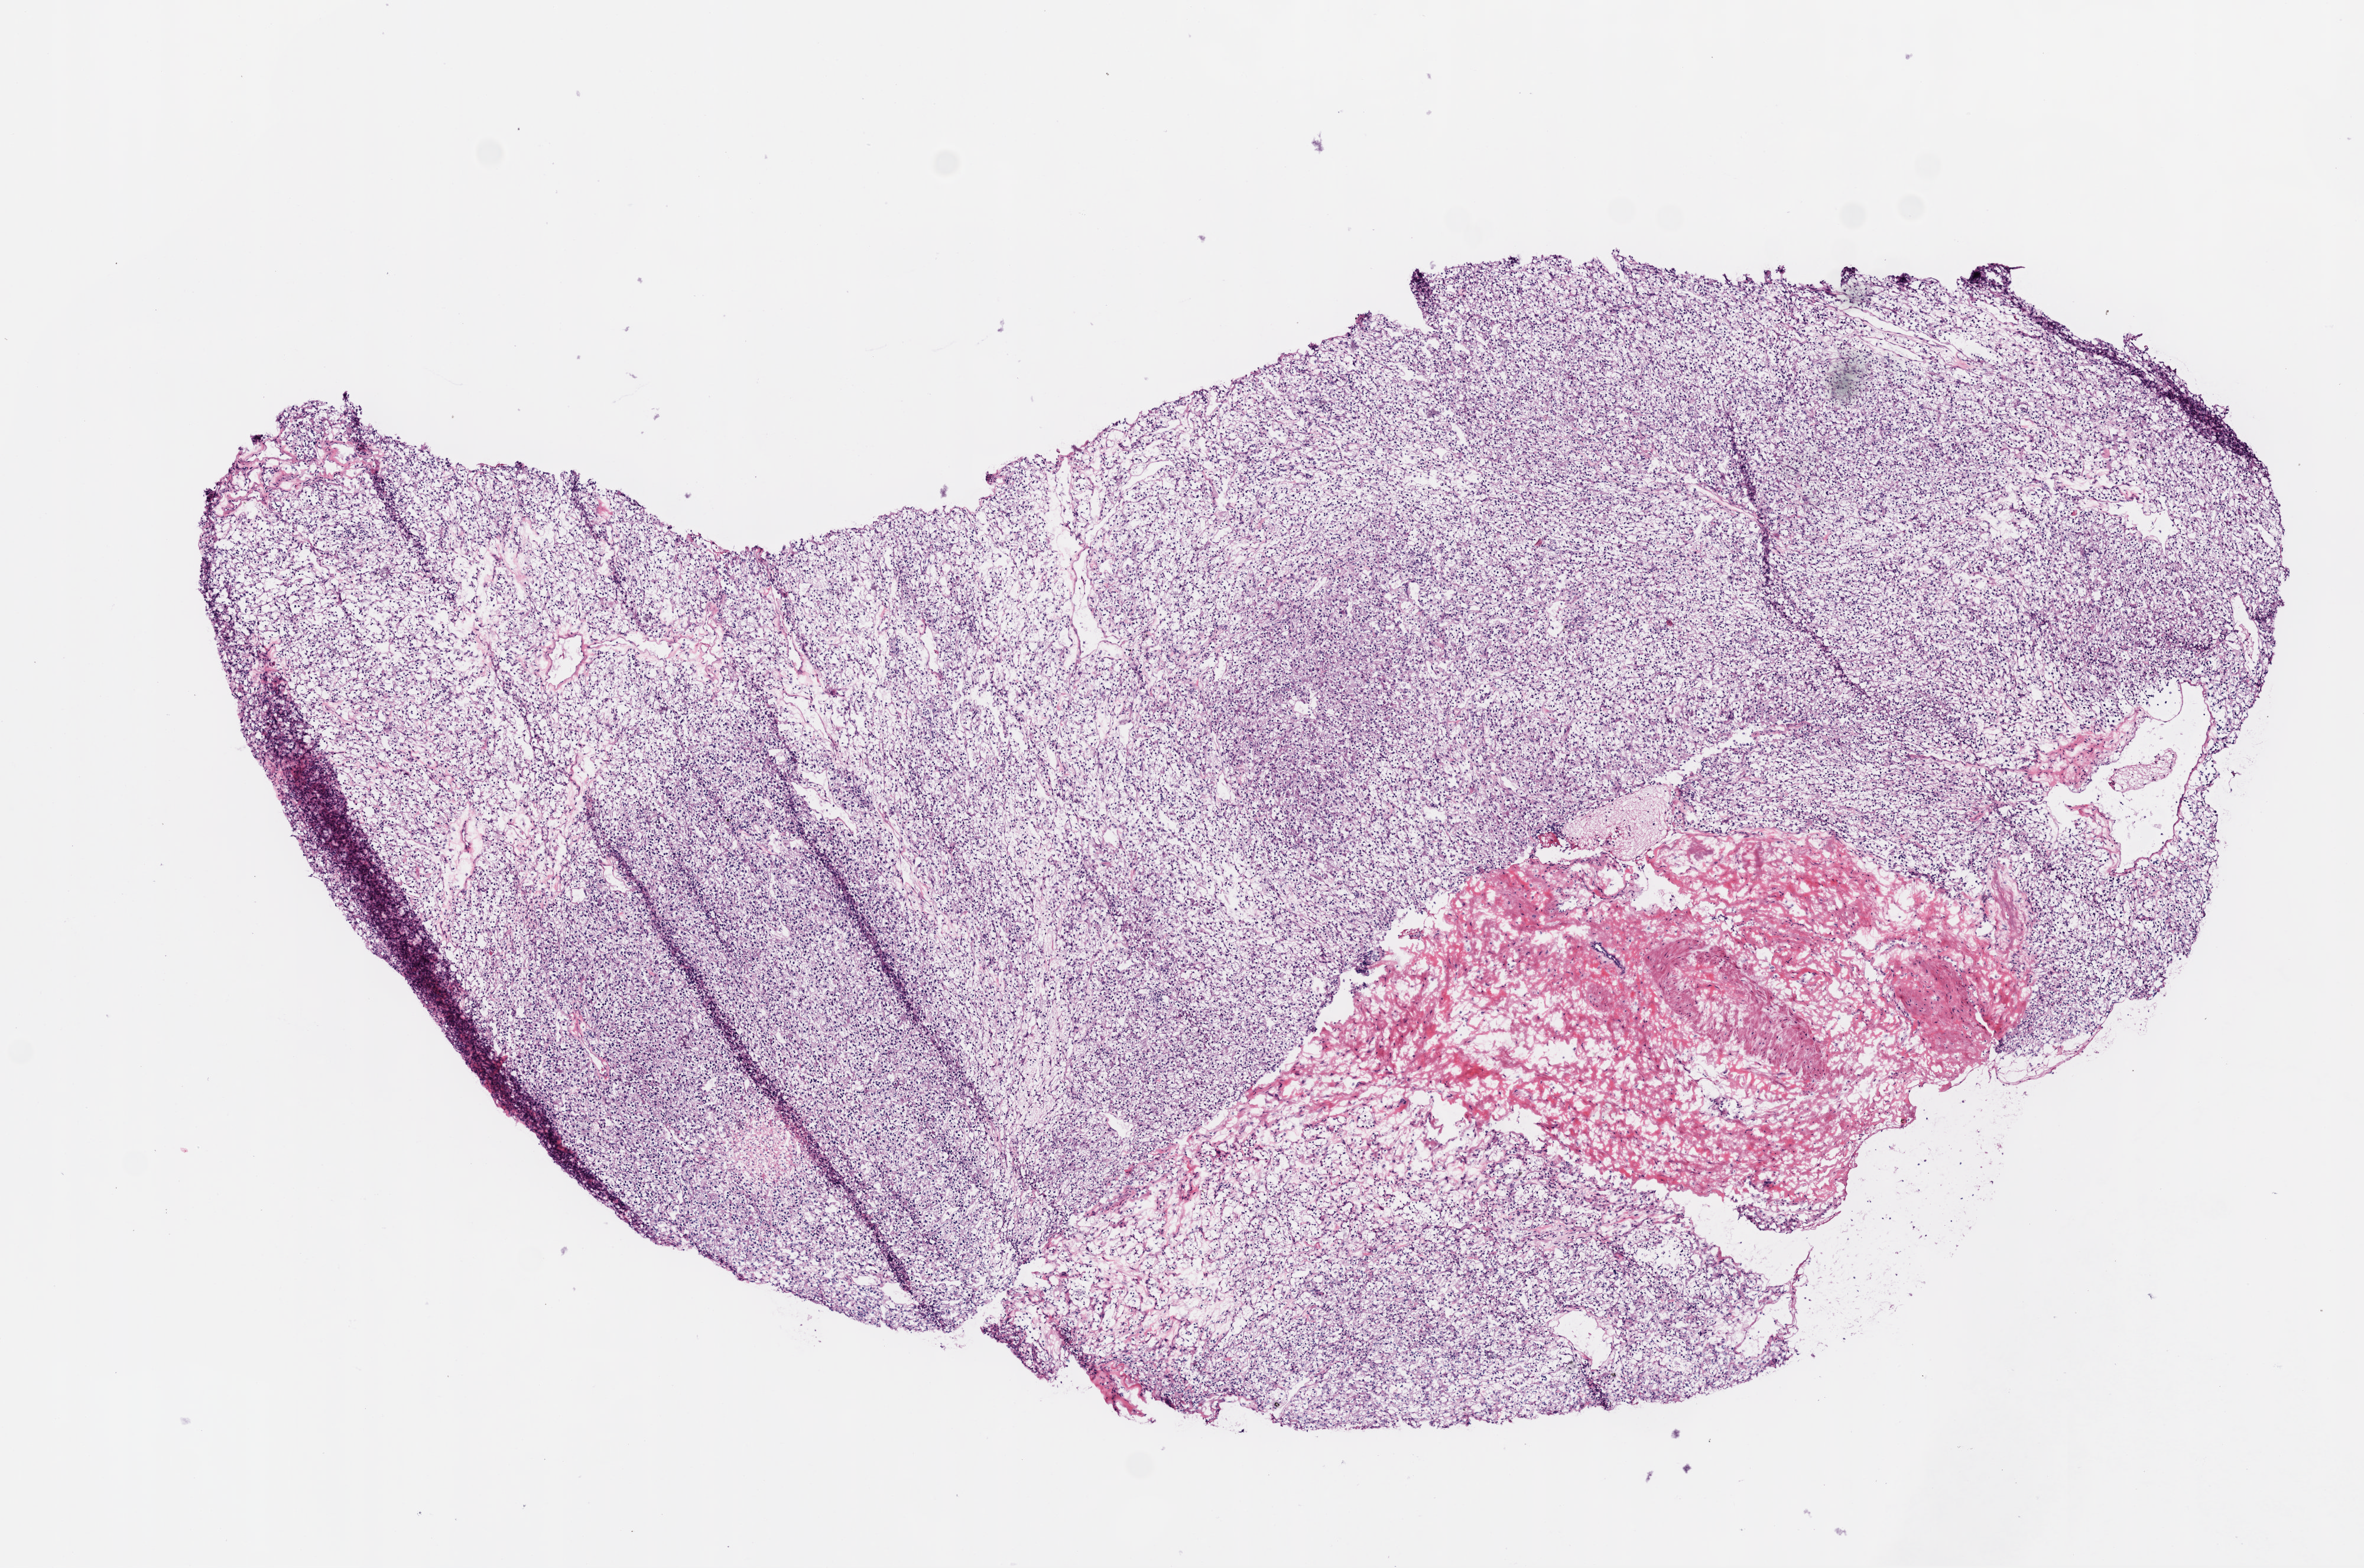
Whole-slide histology image, H&E-stained — whole scanned area (about 8.0 x 5.3 mm, slide scanned at 20x) shown as a low-resolution overview, frozen section from the top of the tissue portion, primary tumour sample from the kidney. Male, age 66 years at initial diagnosis. Histologic grade: G3 (poorly differentiated). Composition of this section per pathologist review: tumour cells 85%, tumour nuclei 90%, normal cells 10%, stromal cells 5%, necrosis 0%.
AJCC pathologic stage: III. Pathologic diagnosis: Clear cell adenocarcinoma, NOS.